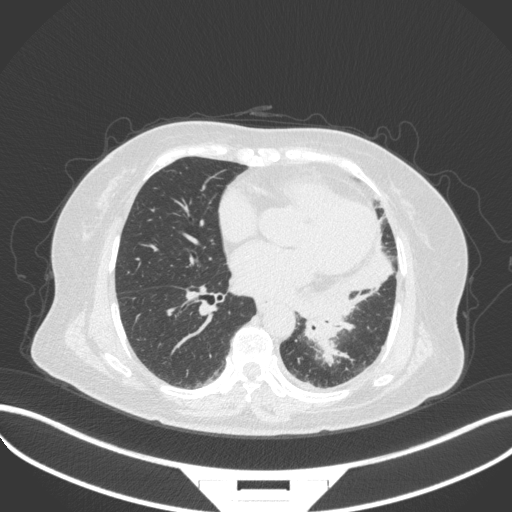
Chest CT, one axial slice. Position 153 of 328 along the scan axis. Reconstruction kernel B31f. 120 kVp. Lung window (W 1500 / L -600 HU). 1 mm slice thickness. 512 × 512 image matrix. Patient: female, 69 years. From the clinical record (not read from this slice): clinical TNM (as recorded): T2b N3 M1.
Annotated regions visible in this slice (bounding box drawn by a radiologist):
- lung tumour (recorded histology: adenocarcinoma): box from (x=298, y=296) to (x=355, y=368) px